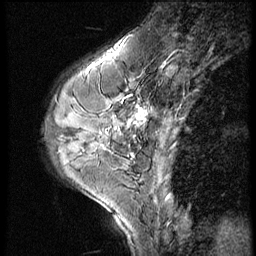
Breast MRI (dynamic contrast-enhanced), one sagittal slice; slice 21 of 56 in the series (ordered by position); 3 images stored at this slice position (order not interpretable as contrast timing); 1.5 T; TE 4.2 ms, TR 9 ms; 2.5 mm slice thickness; 256 × 256 image matrix, field of view 180 × 180 mm. Patient: female, 46 years. Case-level facts recorded for this patient, not image findings: setting: breast cancer imaged before/during neoadjuvant chemotherapy; receptor status: HER2-positive.
Annotated regions visible in this slice (semi-automatic segmentation, software-assisted and operator-edited):
- analysis volume of interest (the breast-tissue region the enhancement analysis was run in; not a lesion): box from (x=73, y=86) to (x=164, y=161) px
- tumour enhancement mask (voxels above the 140 % enhancement threshold inside the analysis volume of interest): (x=127, y=109)–(x=146, y=156)